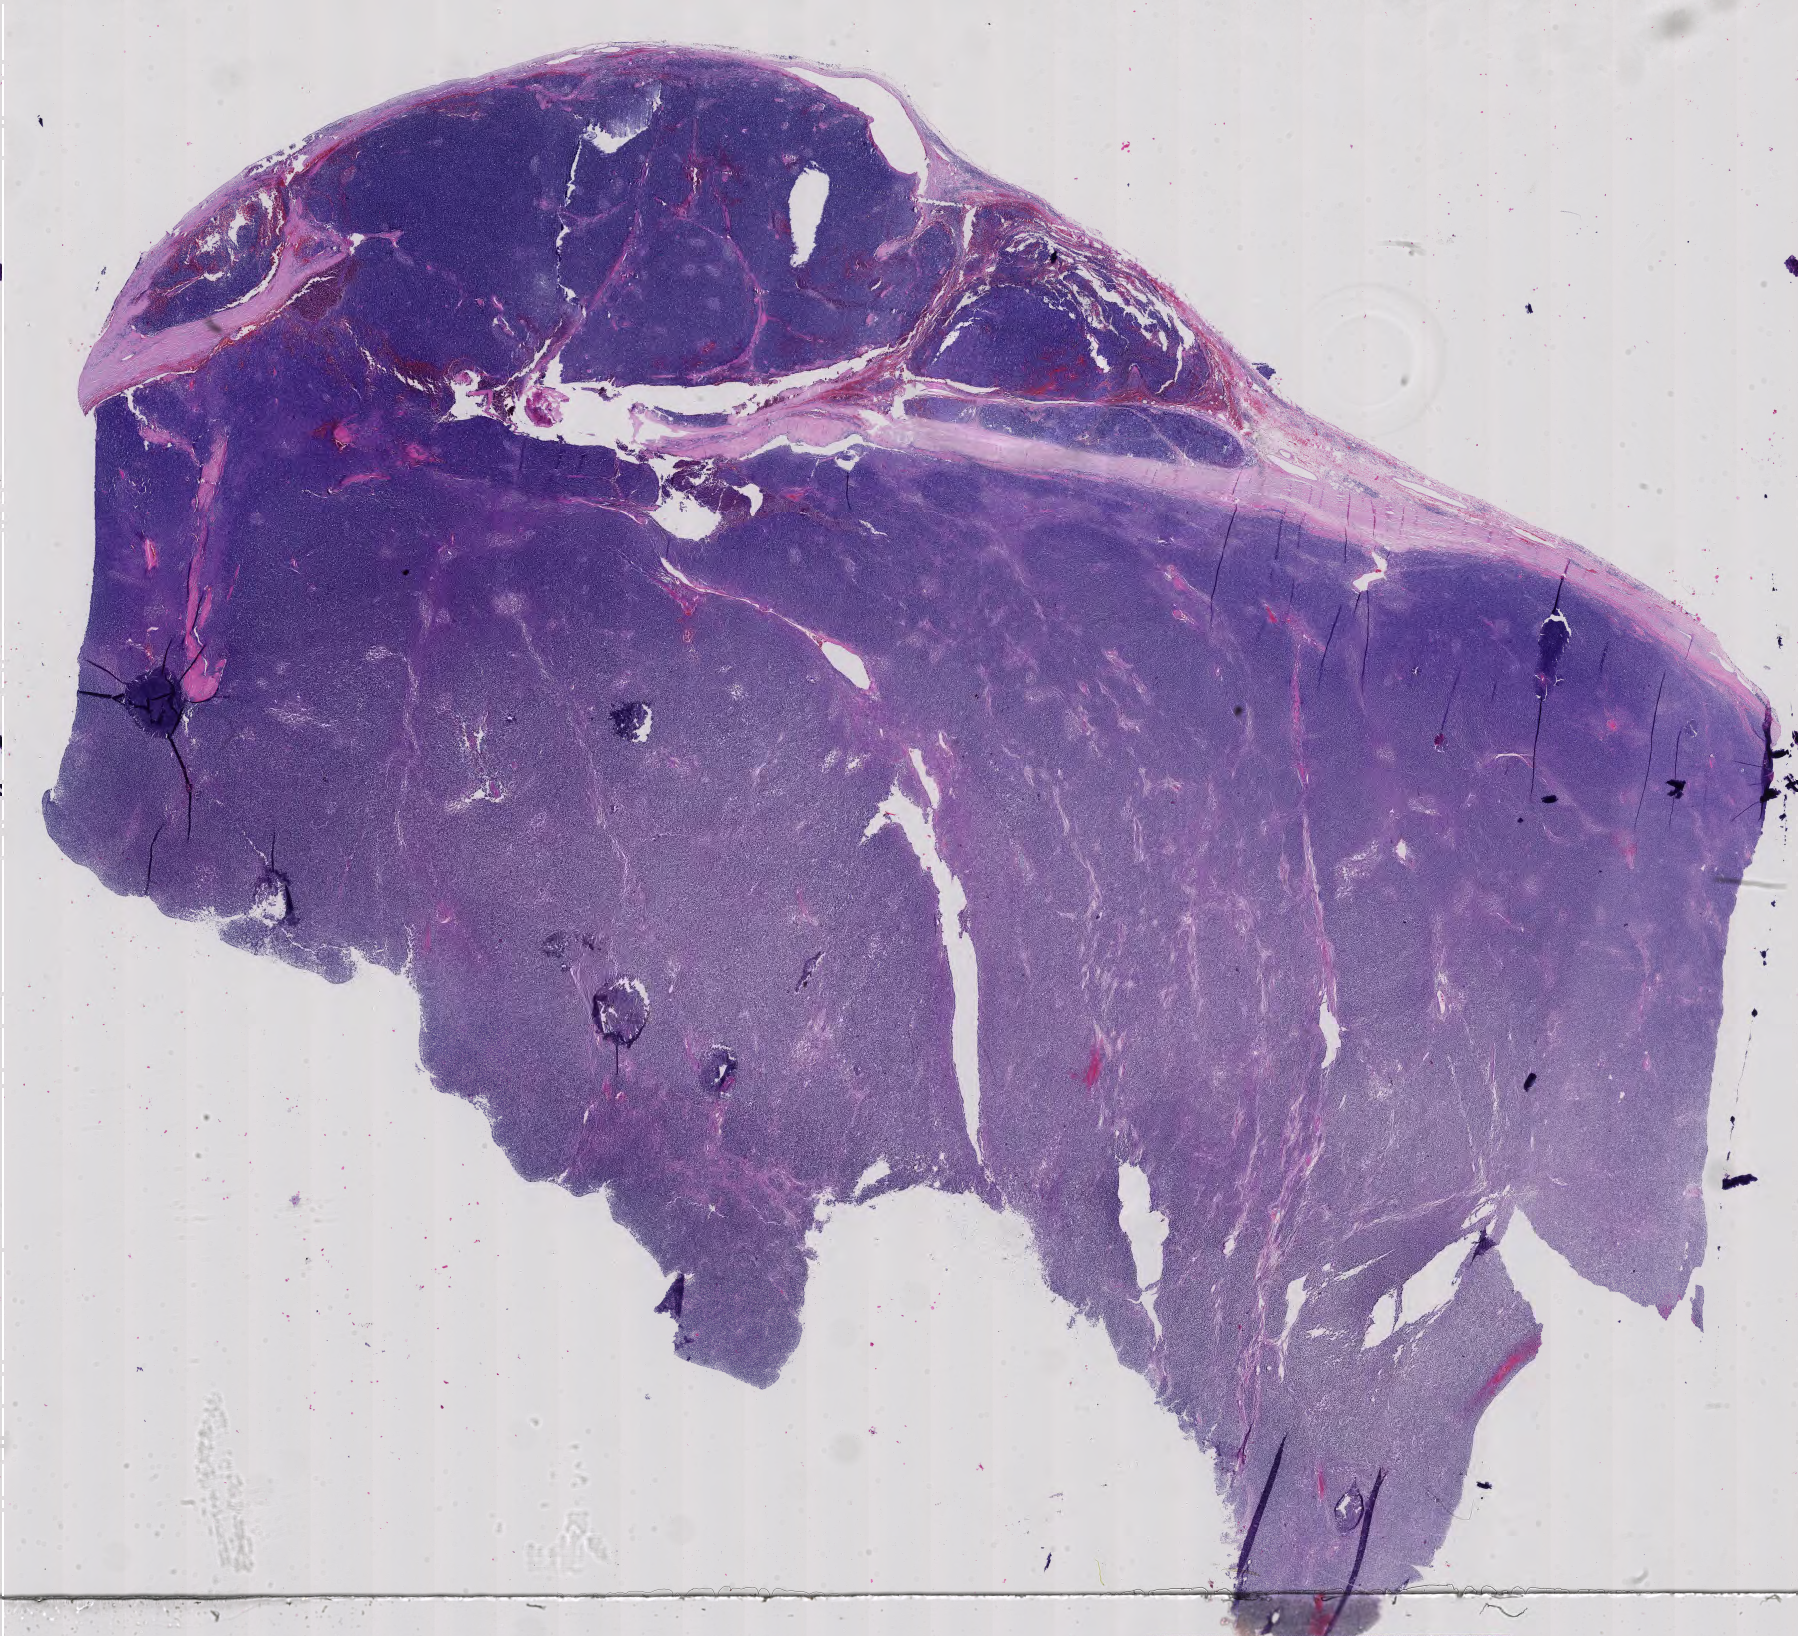
H&E whole-slide image — a low-resolution overview of the entire scanned area, about 26.2 x 23.9 mm (from a 40x scan), formalin-fixed paraffin-embedded (FFPE) diagnostic section, primary tumour sample from the thymus. Male patient; age at initial diagnosis 51 years.
Pathologic diagnosis: Thymoma, type B1, malignant.